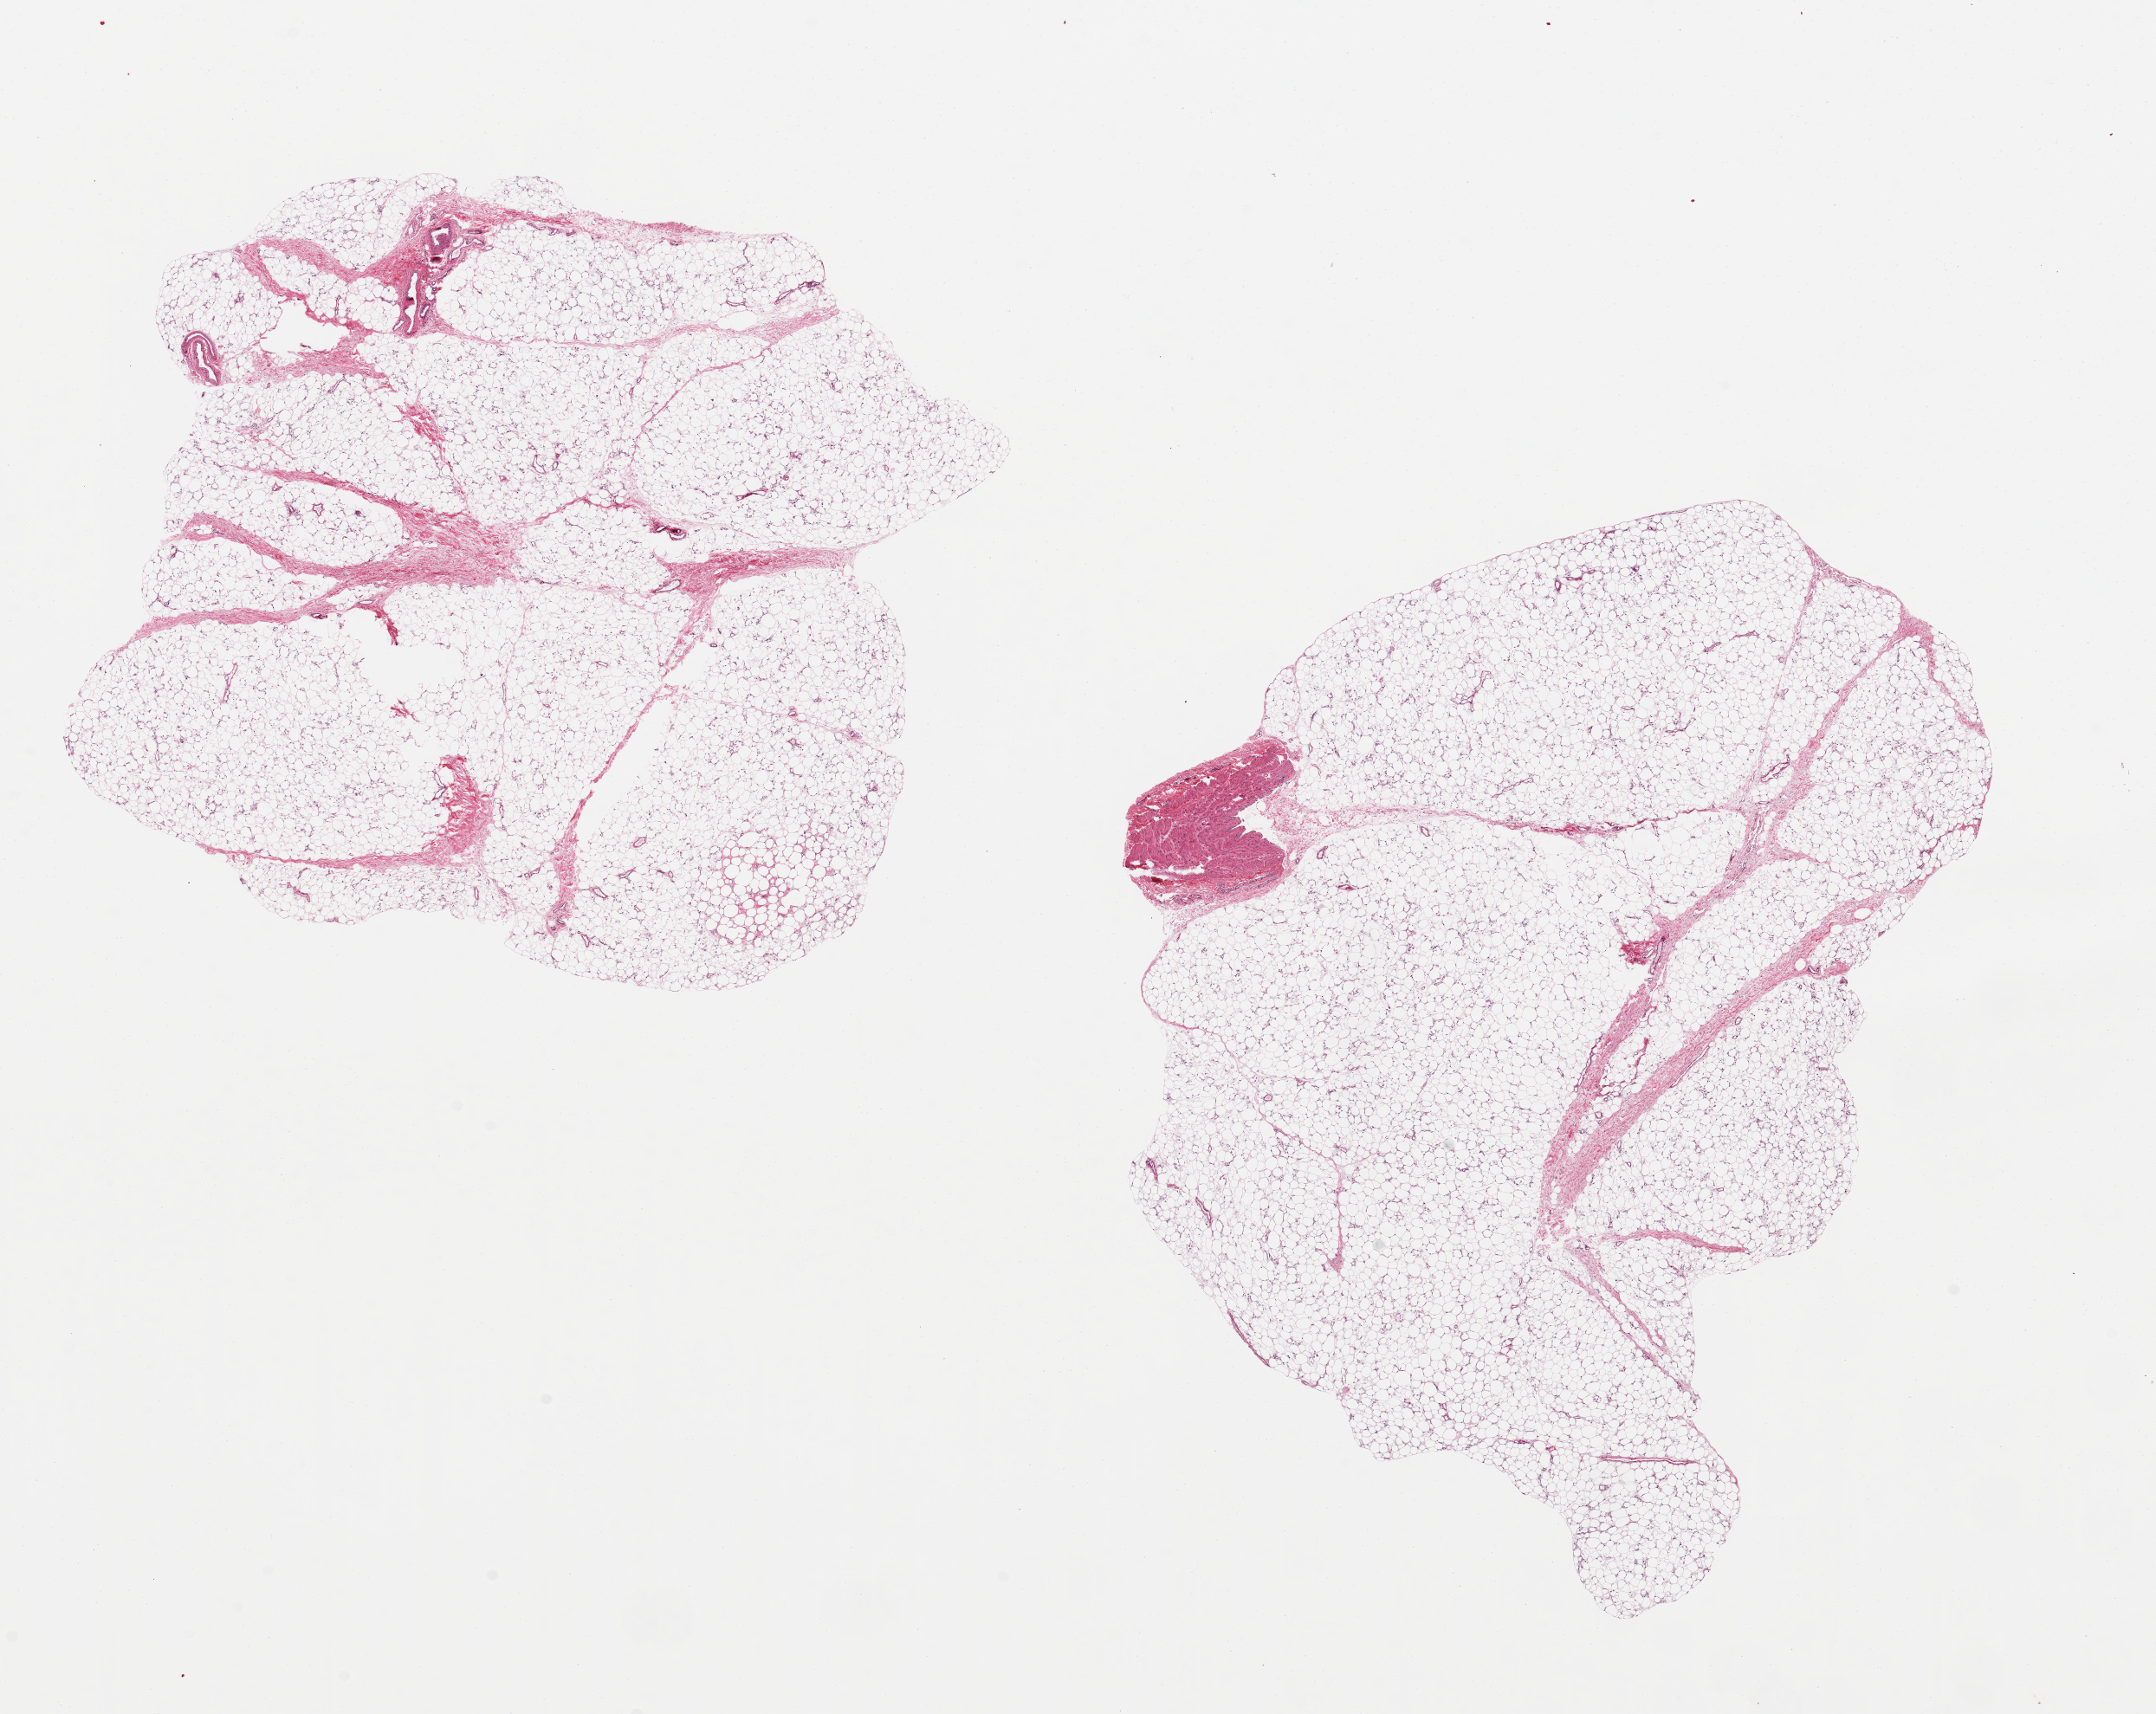
Digitized haematoxylin and eosin-stained section, brightfield, shown as a low-resolution overview of the whole scanned area (about 19.7 x 15.7 mm); PAXgene-fixed paraffin-embedded (PFPE) section; target tissue: adipose tissue; donor tissue sample. Donor sex: female.
Pathologist's review note for this sample: 2 ~8x7mm aliquots, focal areas centrally are under-fixed.